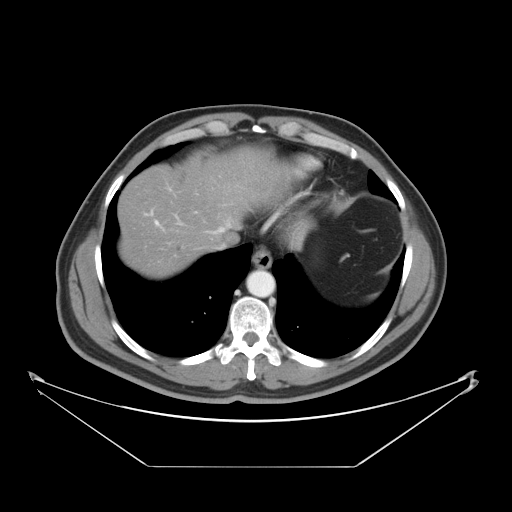
Contrast-enhanced abdominal CT, one axial slice; slice 39 of 46 in the series (ordered by position); 120 kVp; soft-tissue window (W 400 / L 40 HU); 5 mm slice thickness; 512 × 512 image matrix, field of view 465 × 465 mm. Male patient, age 57 years. Case-level facts recorded for this patient, not image findings: diagnosis: colorectal cancer liver metastases, imaged before liver resection; multiple liver metastases: no; largest metastasis: 3.3 cm; disease in both lobes: no.
Outlined on this slice (outlined manually by an expert reader):
- hepatic veins: bounding box <227,221,230,226> (left, top, right, bottom; pixels)
- liver: <119,147,284,278>
- planned liver remnant (the part of the liver to remain after resection): <119,147,283,272>
- portal vein (with intrahepatic branches): <156,221,158,225>